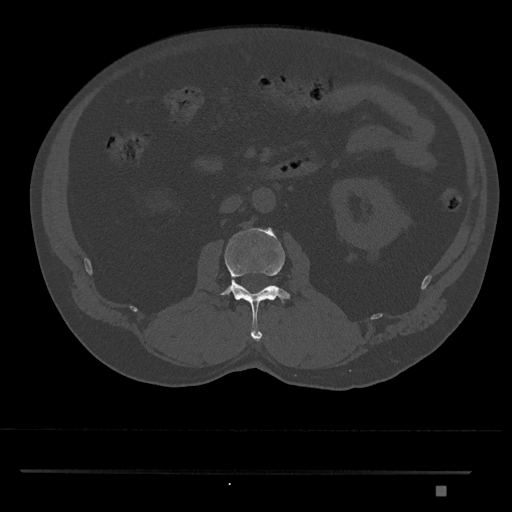
CT including the spine, one axial slice; slice 747 of 1134 in the series (ordered by position); 120 kVp; bone window (W 1800 / L 400 HU); 0.5 mm slice thickness; 512 × 512 image matrix. Male patient, age 65 years. Case-level facts recorded for this patient, not image findings: primary cancer: prostate.
Annotated regions visible in this slice (semi-automatic segmentation, software-assisted and operator-edited):
- L2 vertebra: bounding box [x1, y1, x2, y2] px = [219, 227, 292, 341]